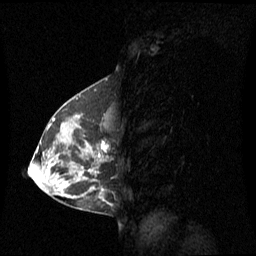
Breast MRI (dynamic contrast-enhanced), one sagittal slice; position 31 of 60 along the scan axis; dynamic contrast-enhanced series, image 2 of 3 at this slice position (ordered by acquisition); 1.5 T; TE 4.2 ms, TR 8.4 ms; 2 mm slice thickness; 256 × 256 image matrix, field of view 270 × 270 mm. Patient: female, 42 years. From the clinical record (not read from this slice): setting: breast cancer imaged before/during neoadjuvant chemotherapy; receptor status: HR-positive, HER2-negative.
Outlined on this slice (semi-automatically segmented with operator editing):
- analysis volume of interest (the breast-tissue region the enhancement analysis was run in; not a lesion): bounding box (x1, y1, x2, y2) in pixels: (56, 114, 110, 185)
- tumour enhancement mask (voxels above the 70 % enhancement threshold inside the analysis volume of interest): (86, 142, 108, 156)